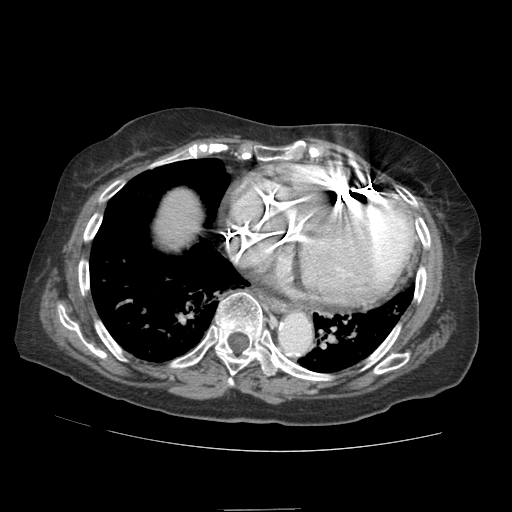
Contrast-enhanced abdominal CT (liver protocol), one axial slice. Position 83 of 89 along the scan axis. 140 kVp. Soft-tissue window (W 400 / L 40 HU). 2.5 mm slice thickness. 512 × 512 image matrix, field of view 360 × 360 mm. From the clinical record (not read from this slice): diagnosis: hepatocellular carcinoma (patient treated with transarterial chemoembolisation; whether this scan precedes or follows treatment is not stated here); TNM stage (as recorded): Stage-II; Child-Pugh class: A; tumour nodularity: multinodular.
Annotated regions visible in this slice (semi-automatically segmented with operator editing):
- abdominal aorta: box from (x=280, y=313) to (x=311, y=353) px
- liver parenchyma outside the tumour (the mass and vessels are separate outlines, so this box may not span the whole liver): (x=154, y=188)–(x=200, y=248)